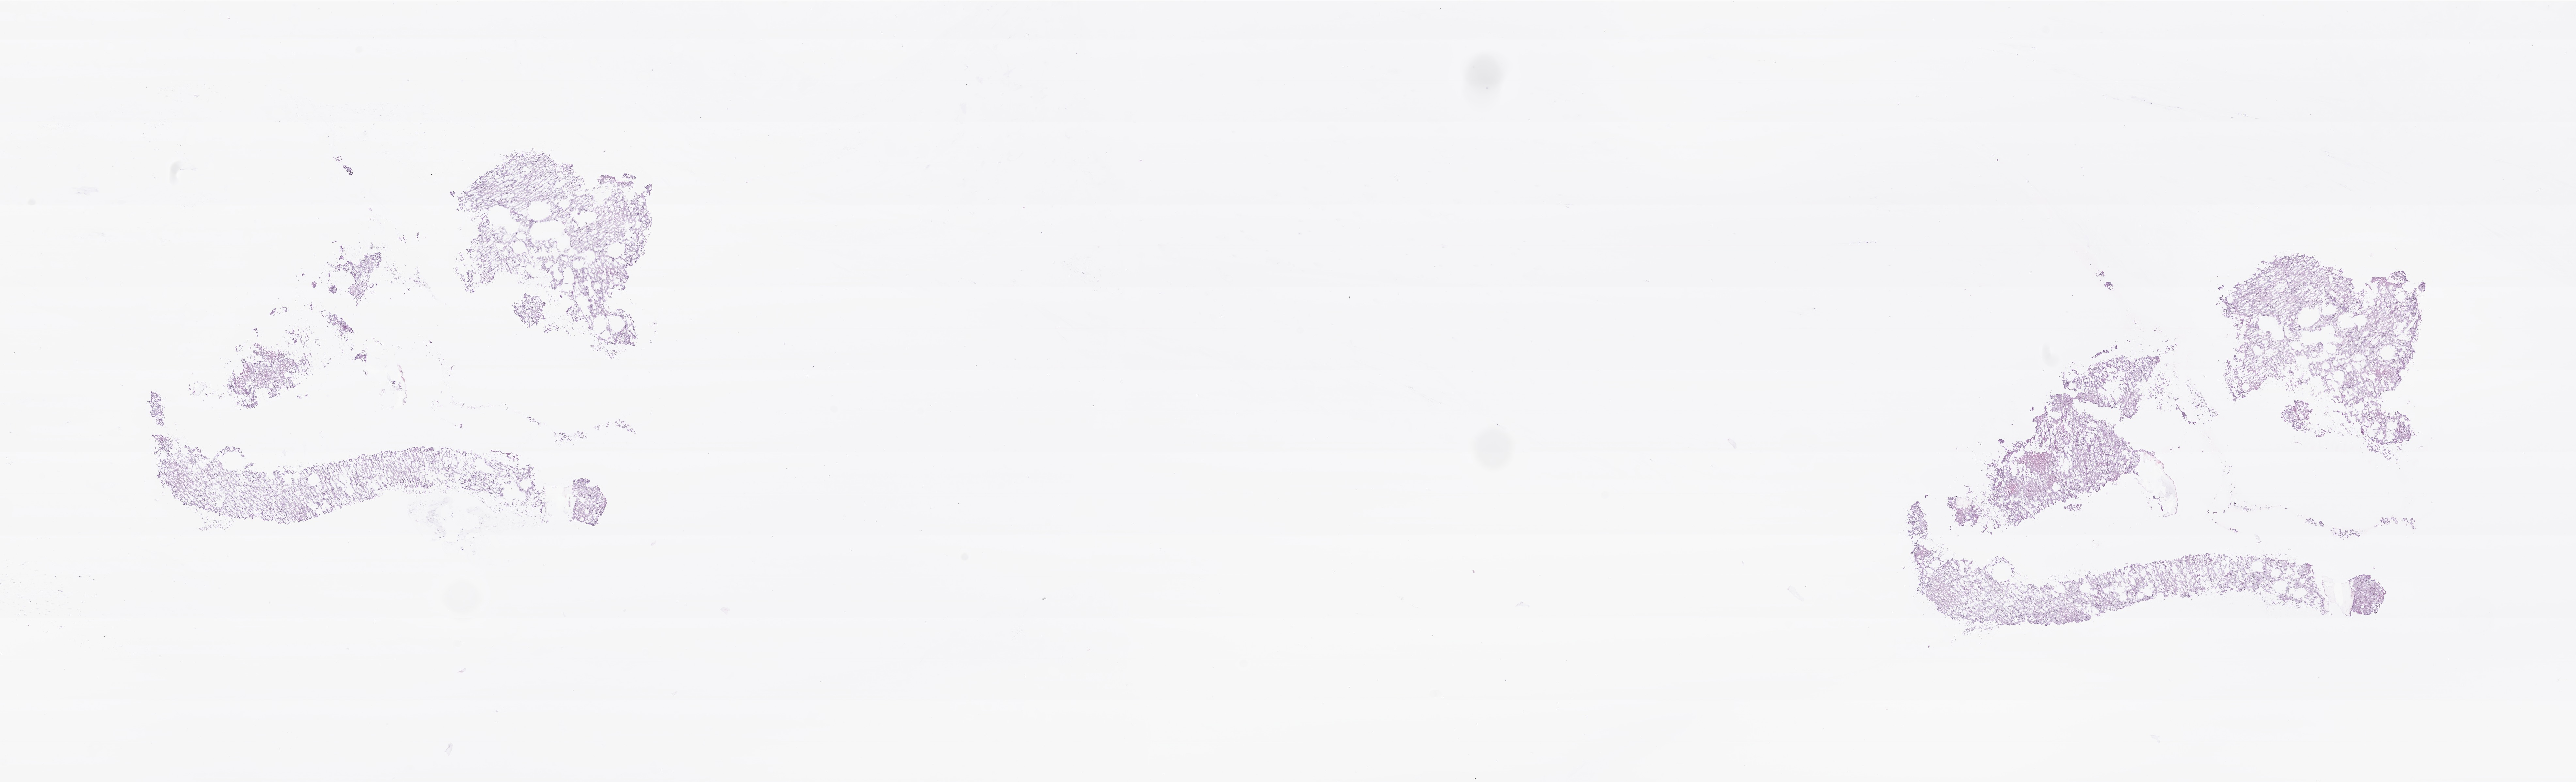
Haematoxylin and eosin whole-slide image of tumor tissue from the brain — shown as a low-resolution overview of the whole scanned area (about 33.2 x 10.1 mm), frozen section (OCT-embedded). Patient female; age 104 months (8 years 8 months).
Diagnosis (ICD-O-3 morphology term): Medulloblastoma, NOS.